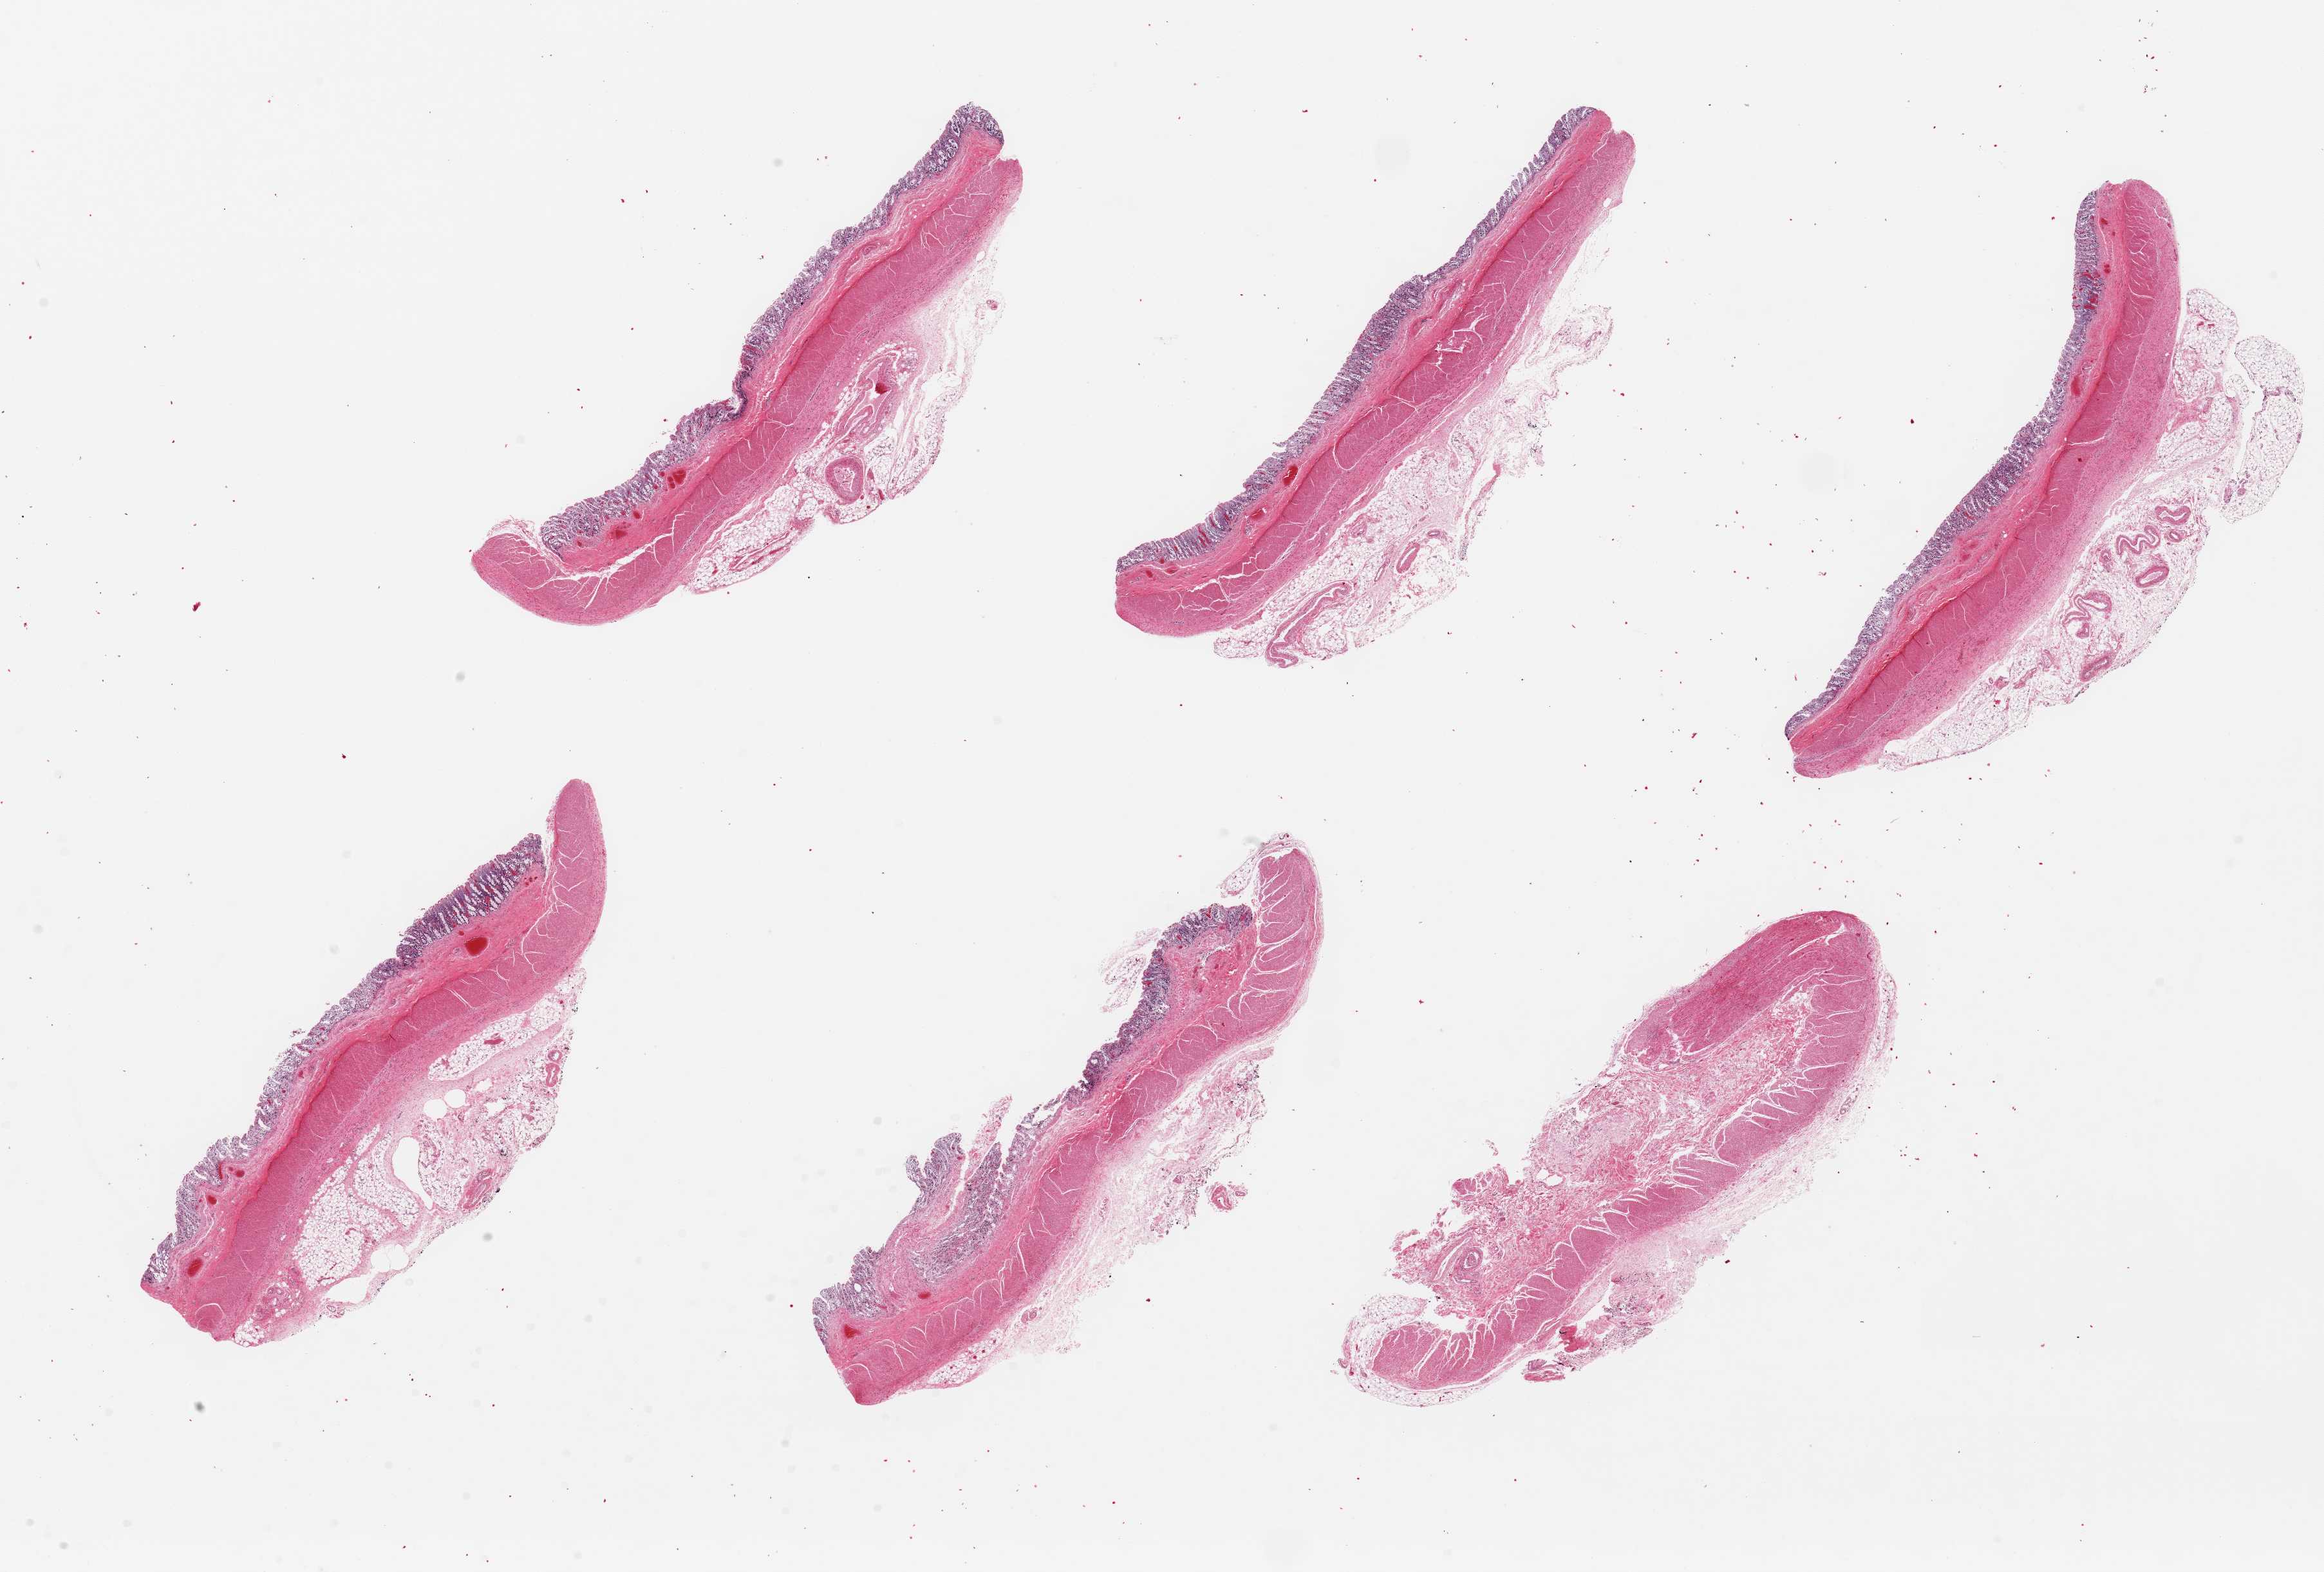
Whole-slide image, haematoxylin and eosin stain, whole scanned area (about 28.5 x 19.3 mm) shown as a low-resolution overview. PAXgene-fixed, paraffin-embedded tissue. Sampled site (target tissue): transverse colon. Tissue donor sample.
Reviewer comment on this tissue sample: 6 pieces up to 8x3mm; mucosa badly autolyzed, ~10% thickness.